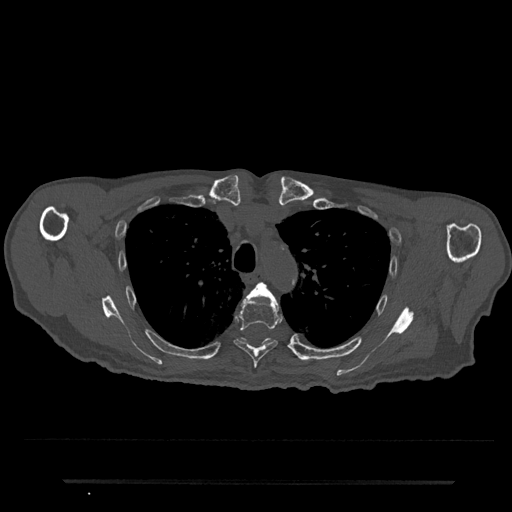
CT including the spine, one axial slice. Slice 578 of 797 in the series (ordered by position). Reconstruction kernel Br40s/3. 120 kVp. Bone window (W 1800 / L 400 HU). 0.5 mm slice thickness. 512 × 512 image matrix, field of view 427 × 427 mm. Patient: male, 74 years. Case-level facts recorded for this patient, not image findings: primary cancer: prostate.
Structures marked on this image (semi-automatic segmentation, software-assisted and operator-edited):
- T4 vertebra: bounding box [x1, y1, x2, y2] px = [248, 282, 275, 299]
- T5 vertebra: [234, 295, 280, 368]
- T6 vertebra: [241, 338, 271, 344]